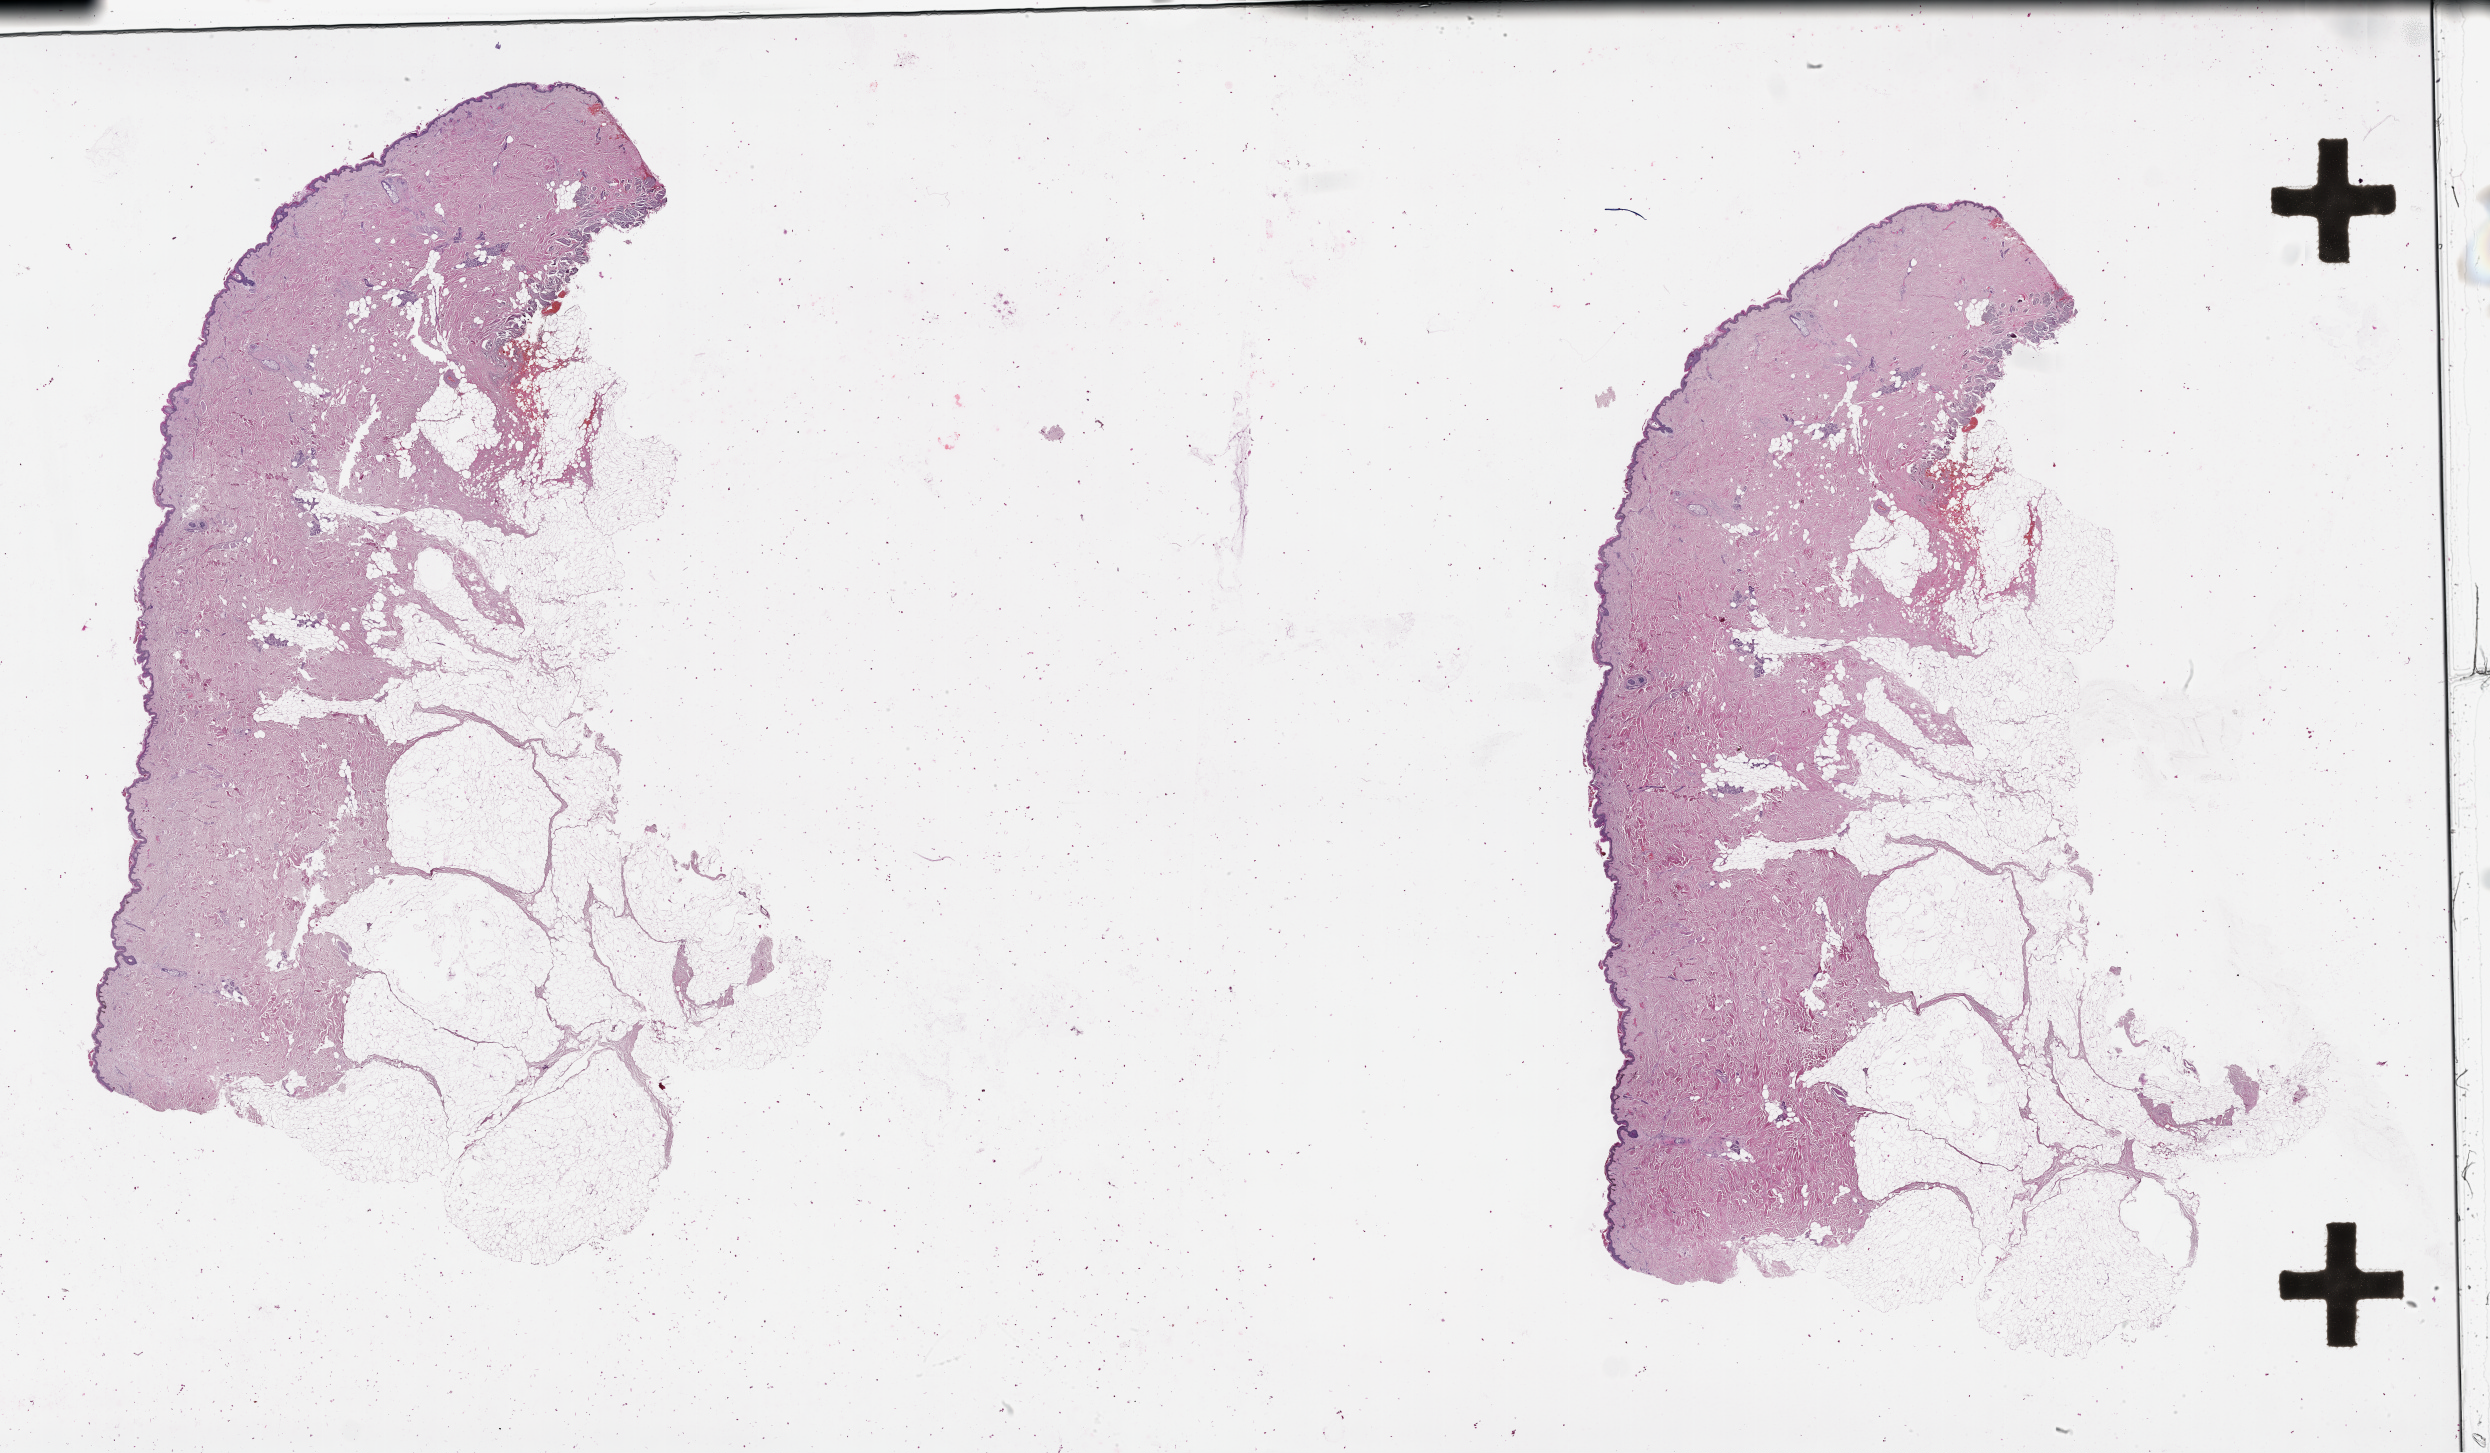
Hematoxylin and eosin (H&E) stained whole-slide image — low-resolution overview of the scanned area, about 40.1 x 23.4 mm. Normal (non-tumour) tissue sample, sampled site: back. Female, 74 y/o.
This section: normal (non-tumour) tissue from the same patient. Patient diagnosis: Malignant melanoma, NOS.